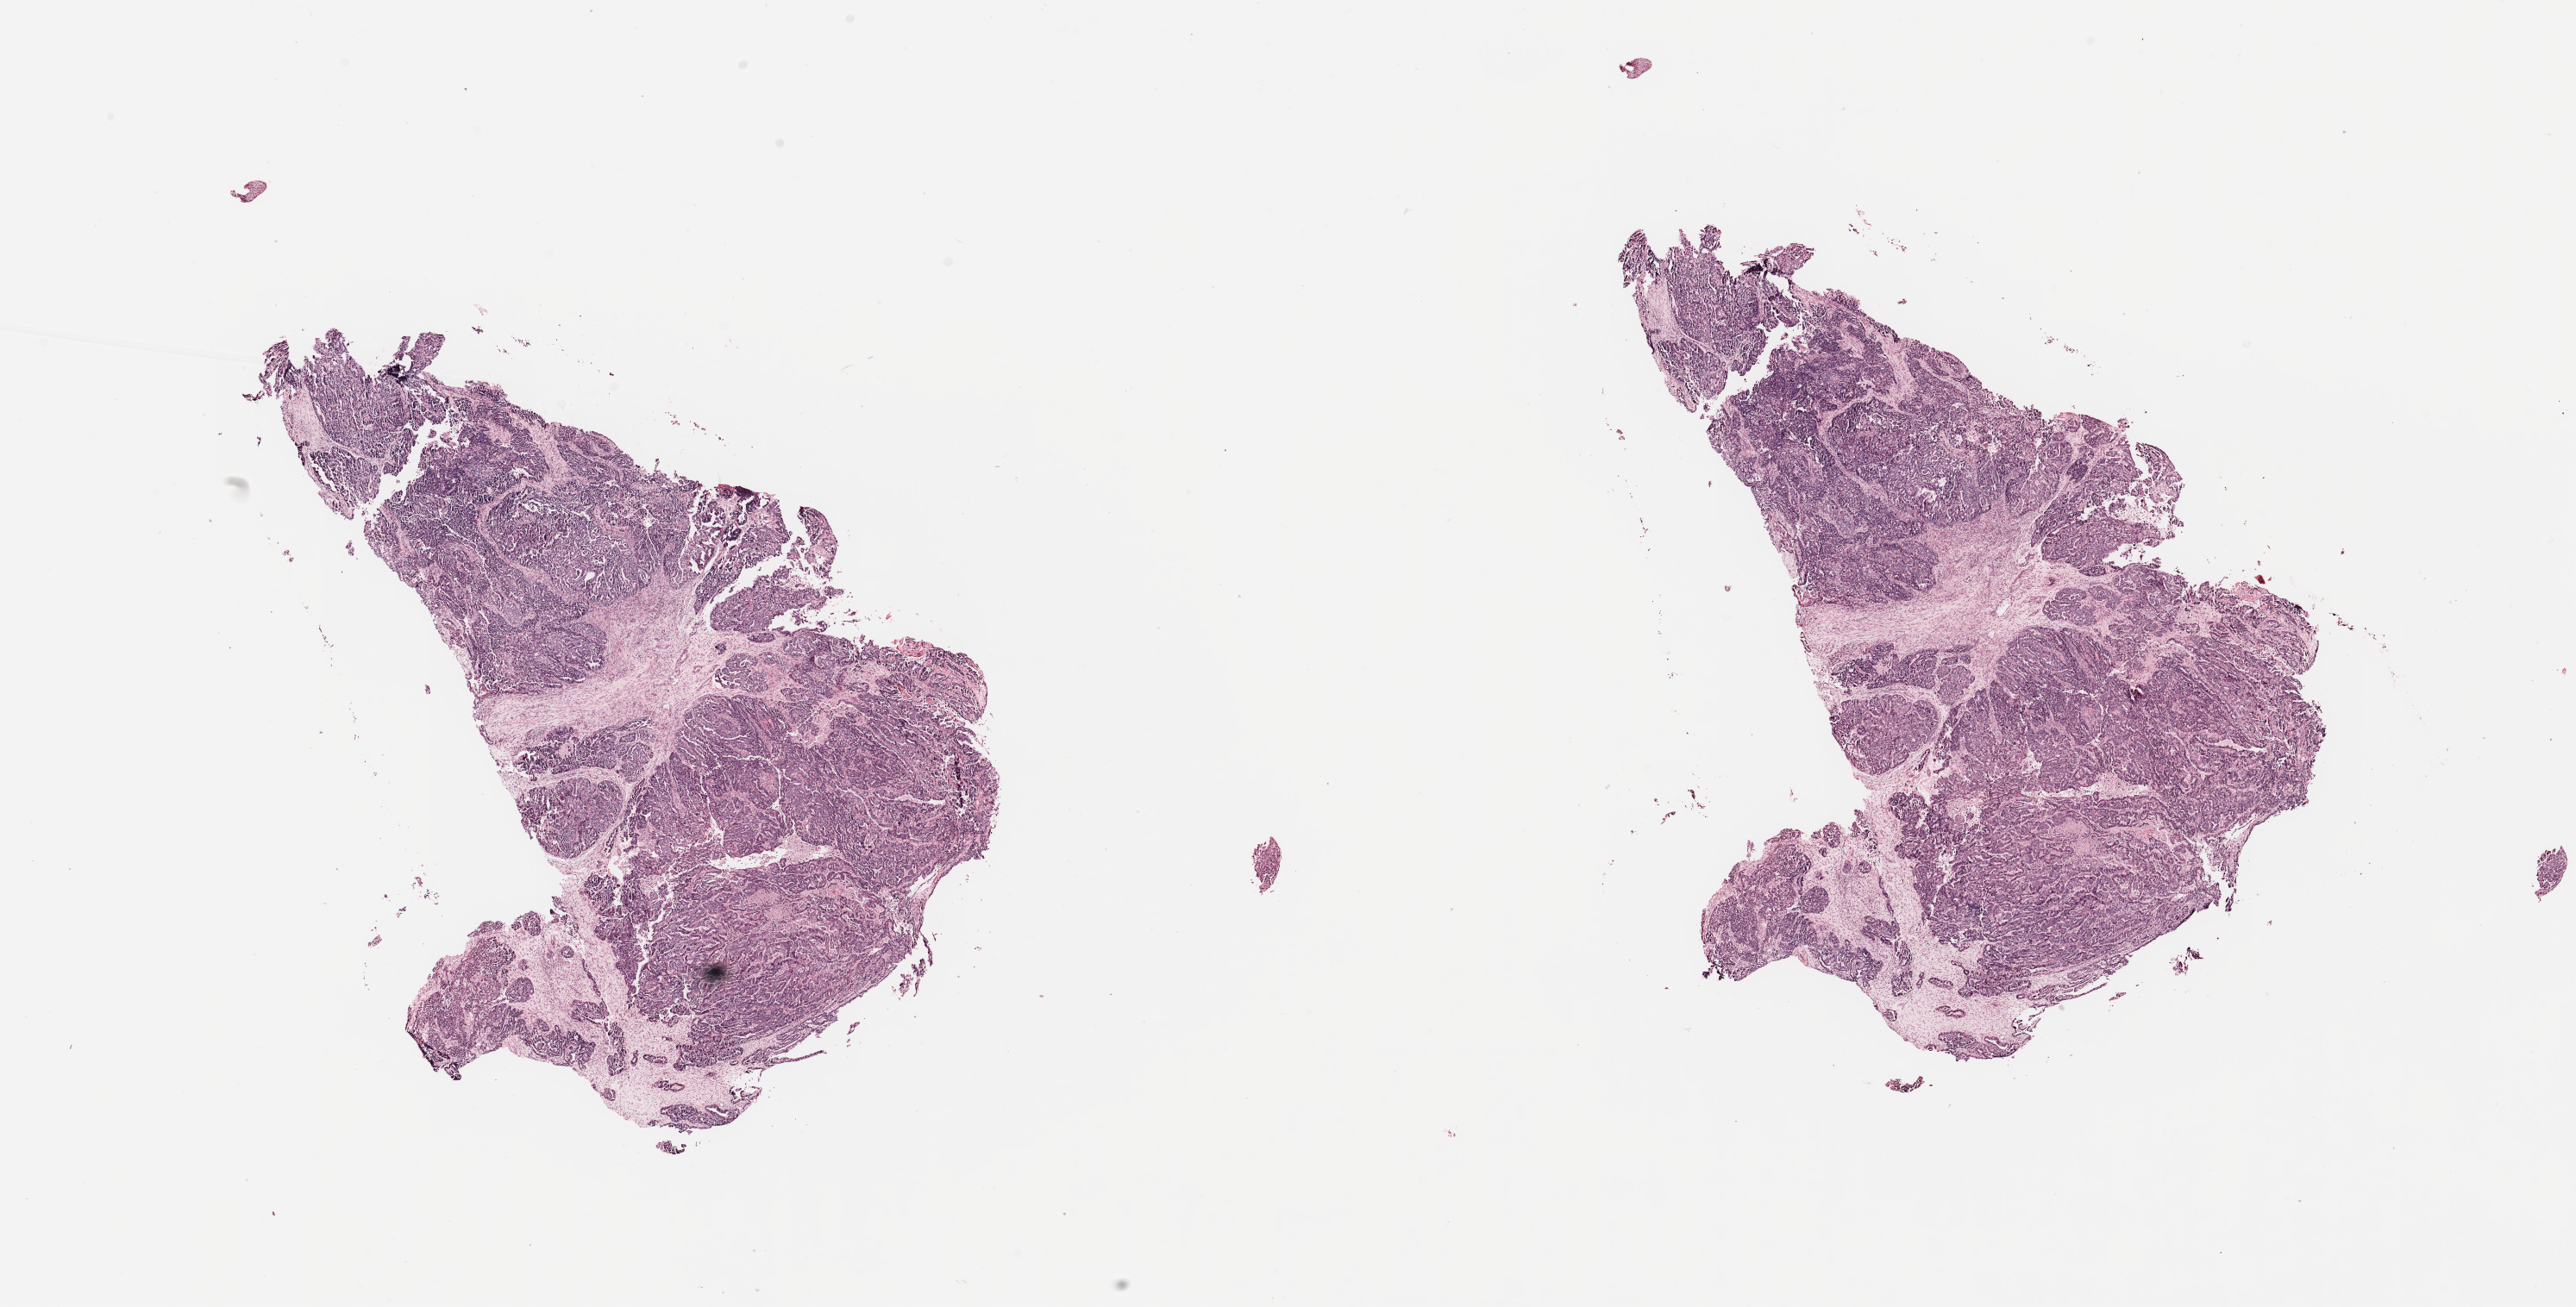
Digitized H&E-stained tissue section (whole slide), low-resolution overview of the scanned area, about 23.6 x 12.0 mm (acquisition: 20x scan), uterus, tumour tissue. 81-year-old female patient.
Patient diagnosis (cohort enrolment): corpus endometrial carcinoma (uterus).